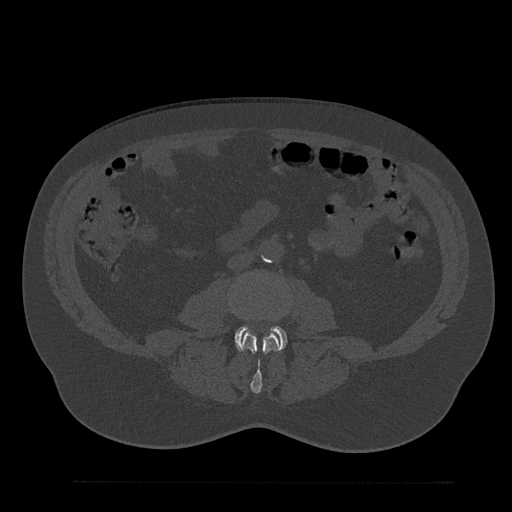
CT including the spine, one axial slice; 120 kVp; bone window (W 1800 / L 400 HU); 0.5 mm slice thickness; 512 × 512 image matrix. Patient: male, 61 years. From the clinical record (not read from this slice): primary cancer: prostate.
Structures marked on this image (semi-automatic segmentation, software-assisted and operator-edited):
- L3 vertebra: bounding box (x1, y1, x2, y2) in pixels: (231, 308, 279, 393)
- L4 vertebra: (235, 326, 287, 350)